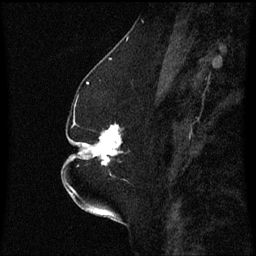
Breast MRI (dynamic contrast-enhanced), one sagittal slice; slice 23 of 60 in the series (ordered by position); dynamic contrast-enhanced series, image 2 of 3 at this slice position (ordered by acquisition); 1.5 T; TE 4.2 ms, TR 8.4 ms; 2.3 mm slice thickness; 256 × 256 image matrix, field of view 200 × 200 mm. Patient: female, 52 years. From the clinical record (not read from this slice): setting: breast cancer imaged before/during neoadjuvant chemotherapy; receptor status: HR-positive, HER2-negative.
Outlined on this slice (semi-automatic segmentation, software-assisted and operator-edited):
- analysis volume of interest (the breast-tissue region the enhancement analysis was run in; not a lesion): bounding box (x1, y1, x2, y2) in pixels: (75, 124, 129, 181)
- tumour enhancement mask (voxels above the 70 % enhancement threshold inside the analysis volume of interest): (75, 126, 122, 167)